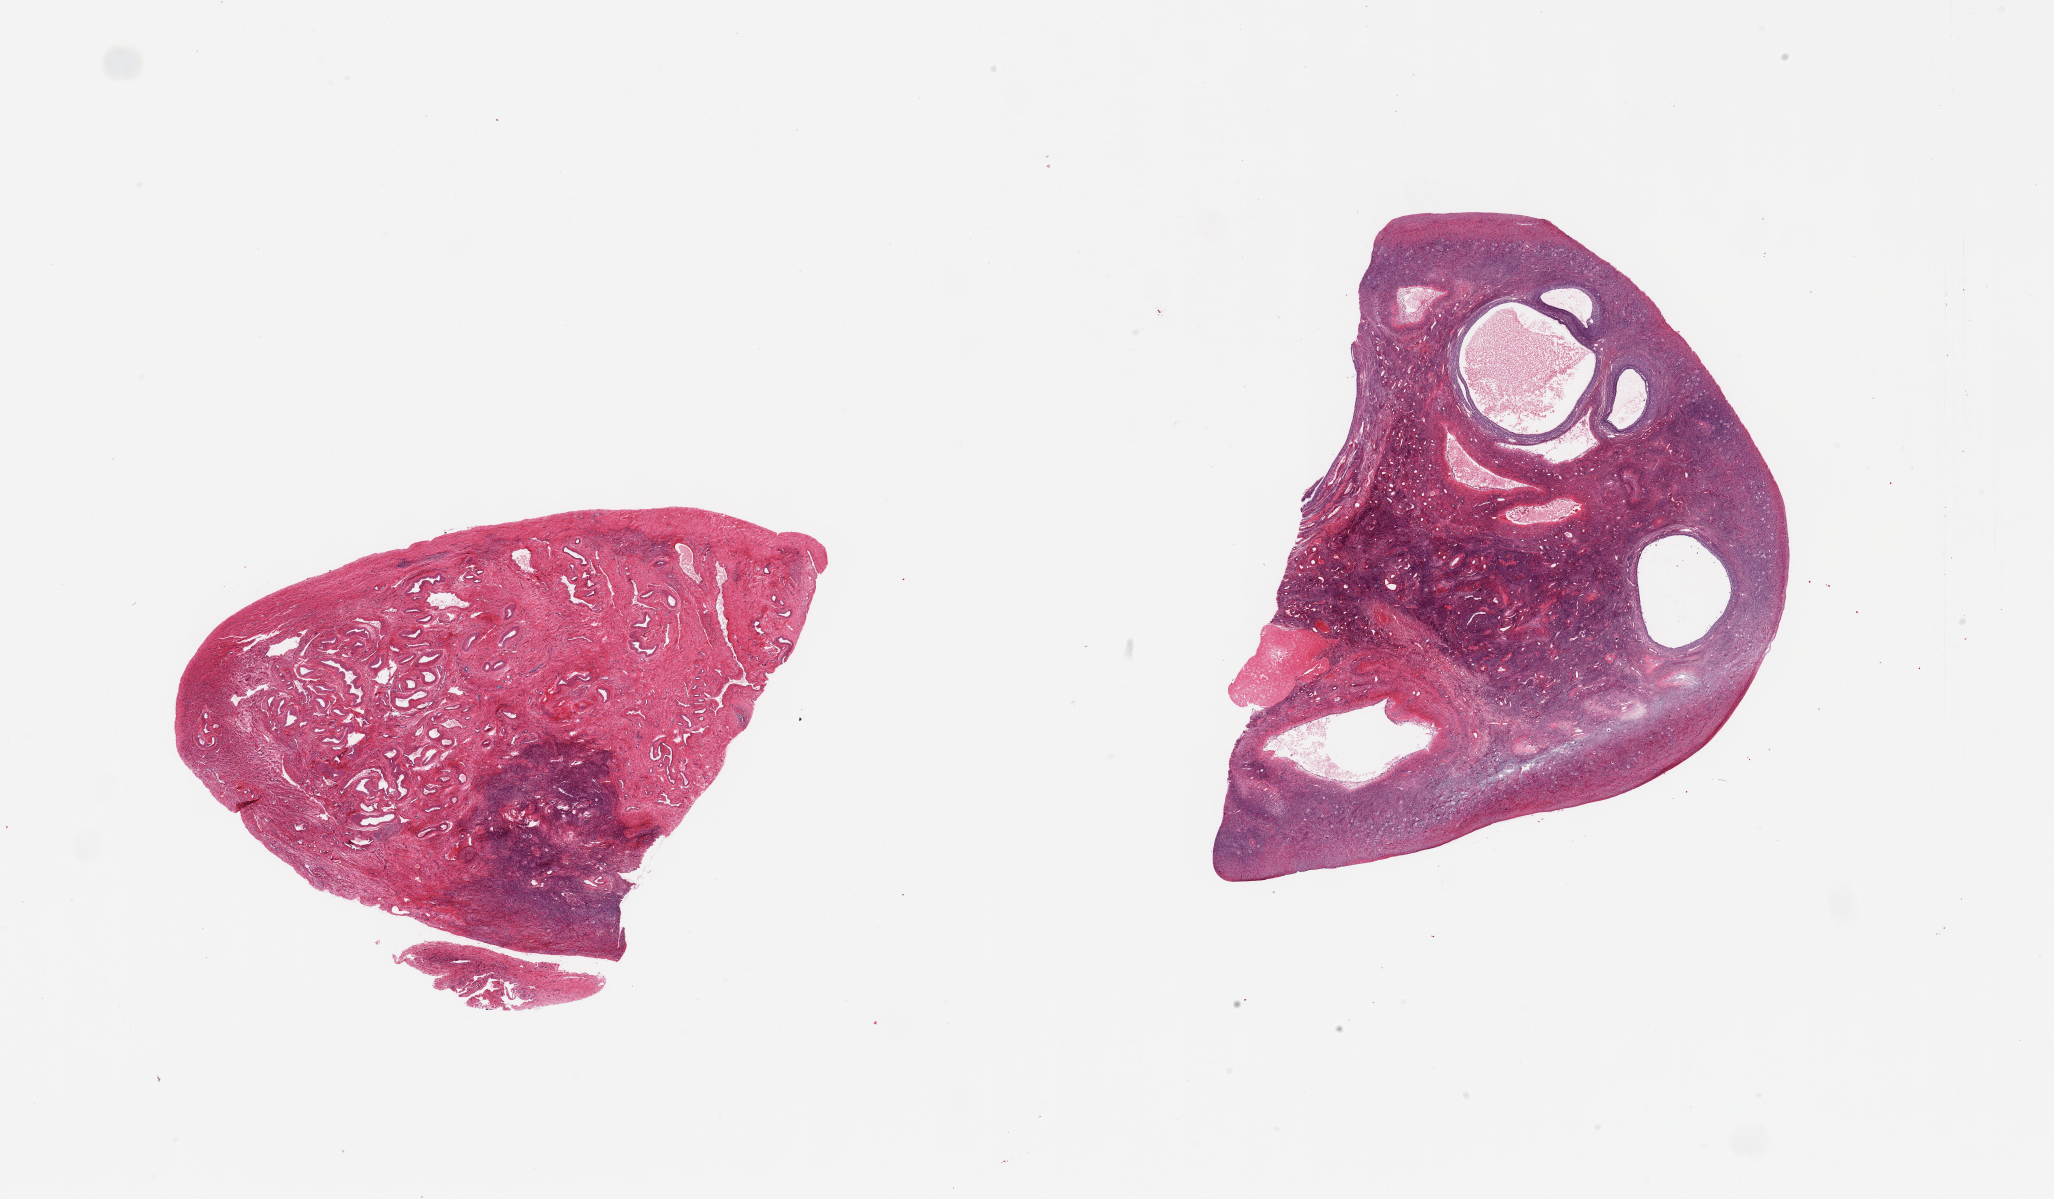
Digitized haematoxylin and eosin-stained section, brightfield, shown as a low-resolution overview of the whole scanned area (about 32.5 x 19.0 mm, slide scanned at 20x). PAXgene-fixed, paraffin-embedded tissue. Sampled site (target tissue): ovary. Donor tissue sample. Donor sex: female.
• review note (as recorded): 2 pieces, one largely hilum; Well-preserved oocyctes; aggregates; follicular cysts